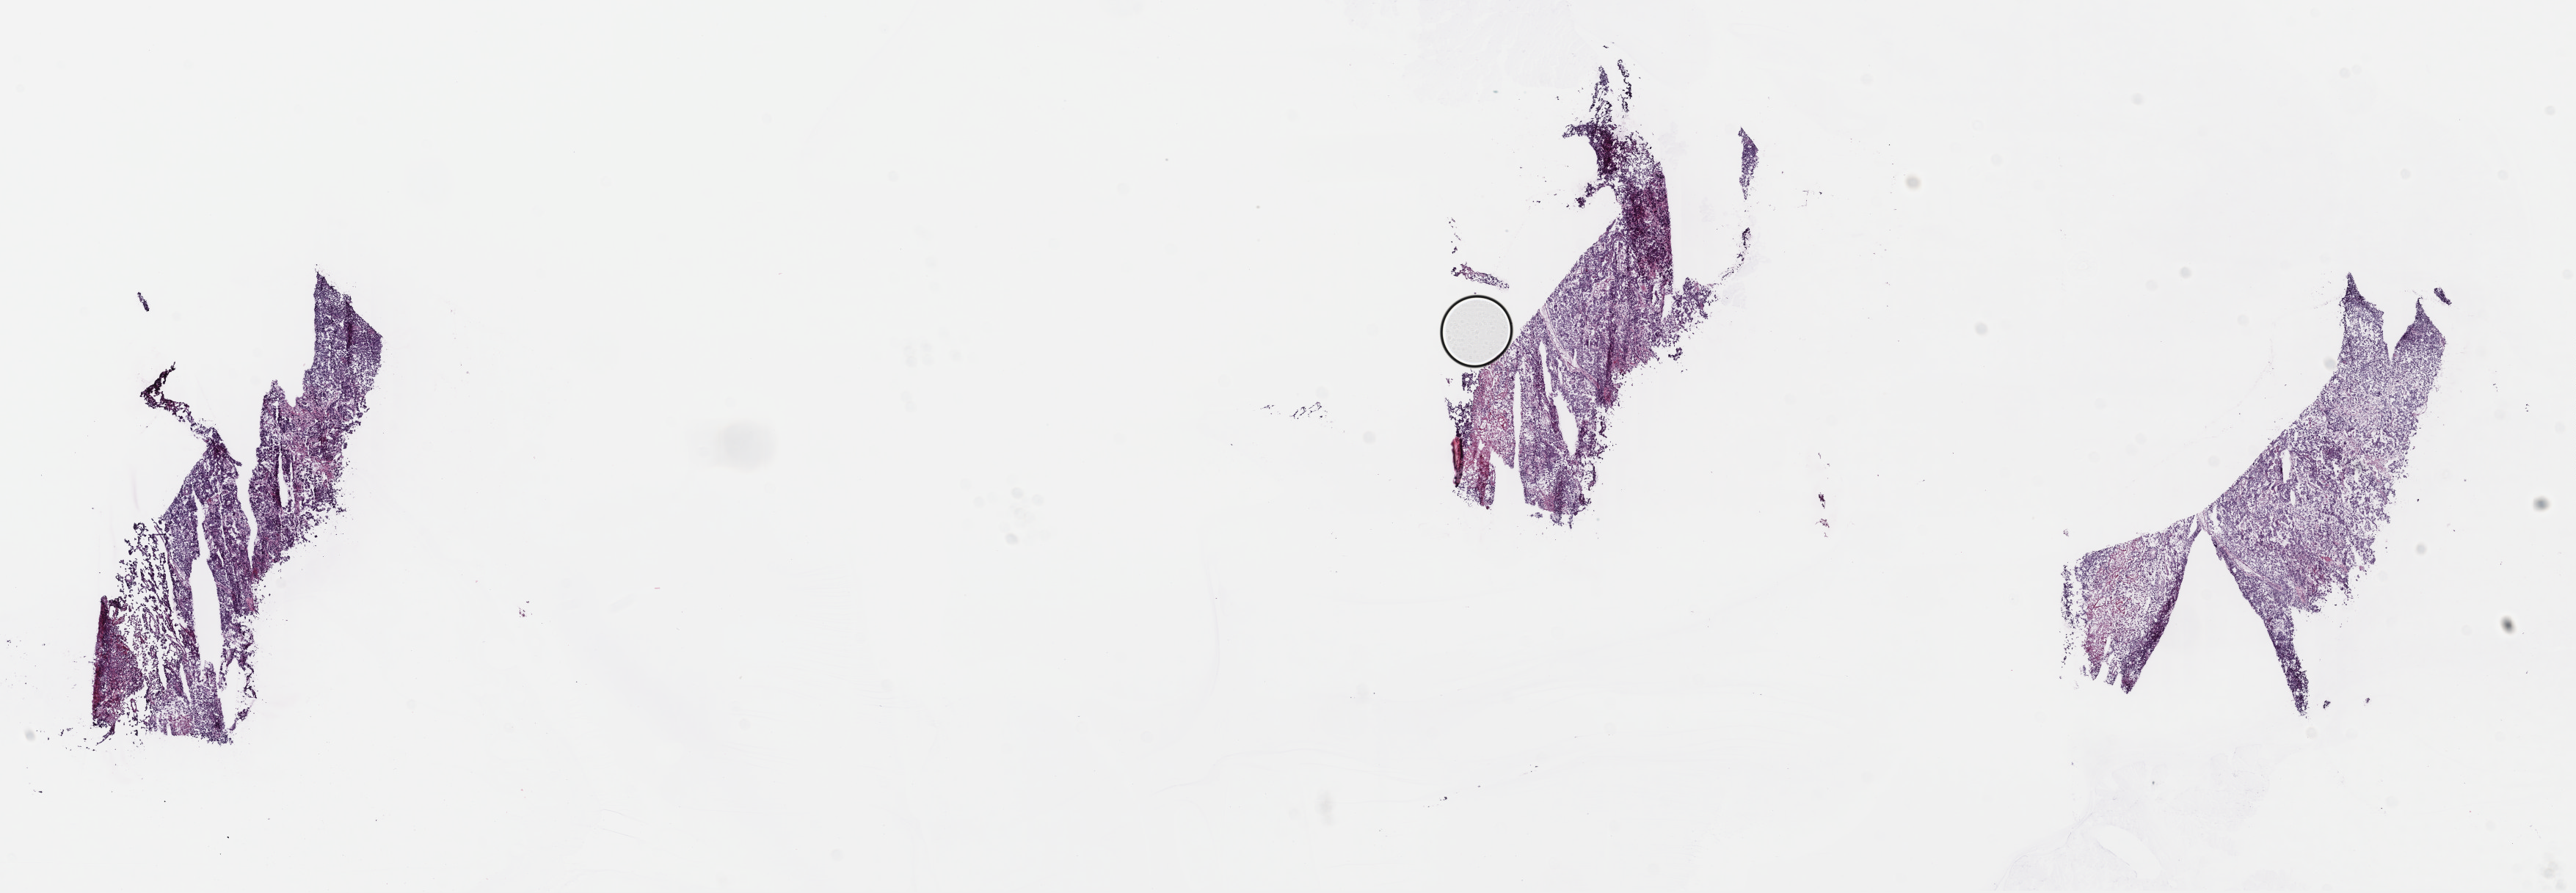
Whole-slide histology image, H&E, whole scanned area (about 27.6 x 9.6 mm) shown as a low-resolution overview; frozen section from the top of the tissue portion; sample: primary tumour, uterus. Female, age 71 years at initial diagnosis. Slide review estimates, as recorded: tumour cells 98%, tumour nuclei 85%, normal cells 0%, stromal cells 0%, necrosis 2%. Infiltration values recorded for this section: lymphocyte infiltration 1%, monocyte infiltration 0%, neutrophil infiltration 0%.
FIGO stage: IA. Pathologic diagnosis: Carcinosarcoma, NOS (endometrium).